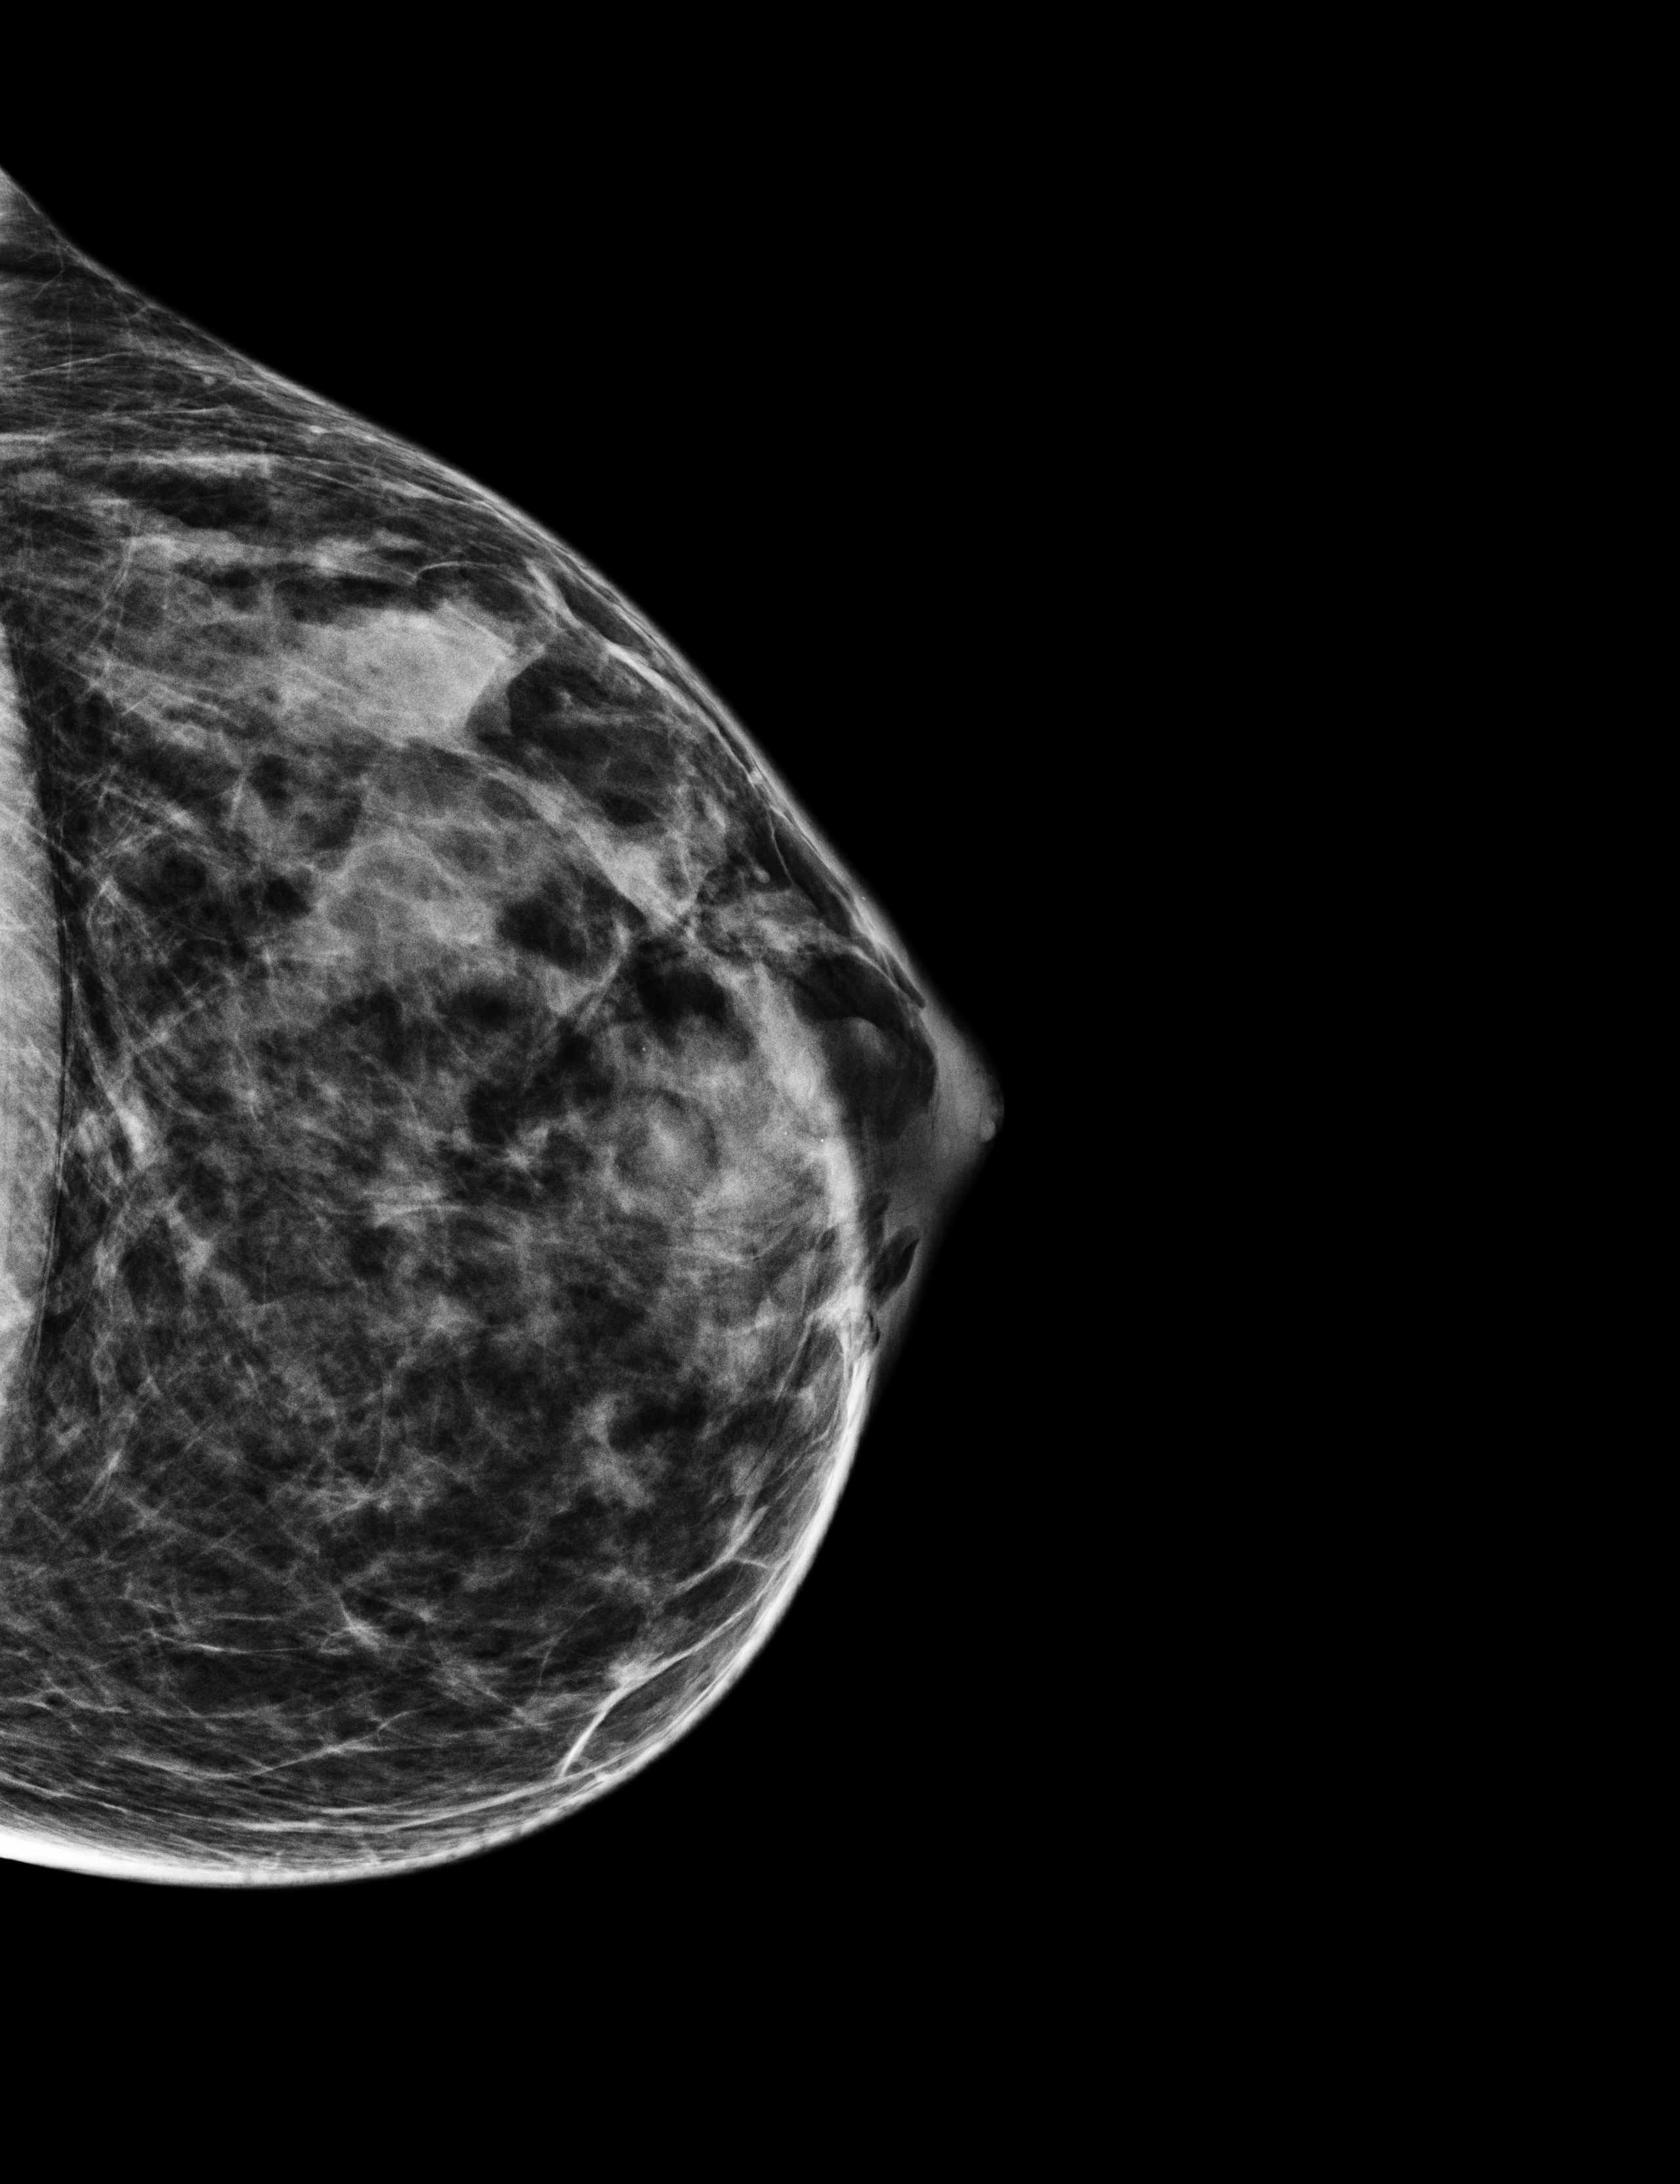
Digital mammogram (FFDM); left breast; cranio-caudal projection; annual screening mammography examination; system: Selenia Dimensions. Patient aged 44 years (female).
Breast density at the screening exam (both breasts): heterogeneously dense (BI-RADS density category c). Final BI-RADS category for the screening round (tomosynthesis exam, both breasts): category 2. Recall: recalled for additional imaging after this screen.